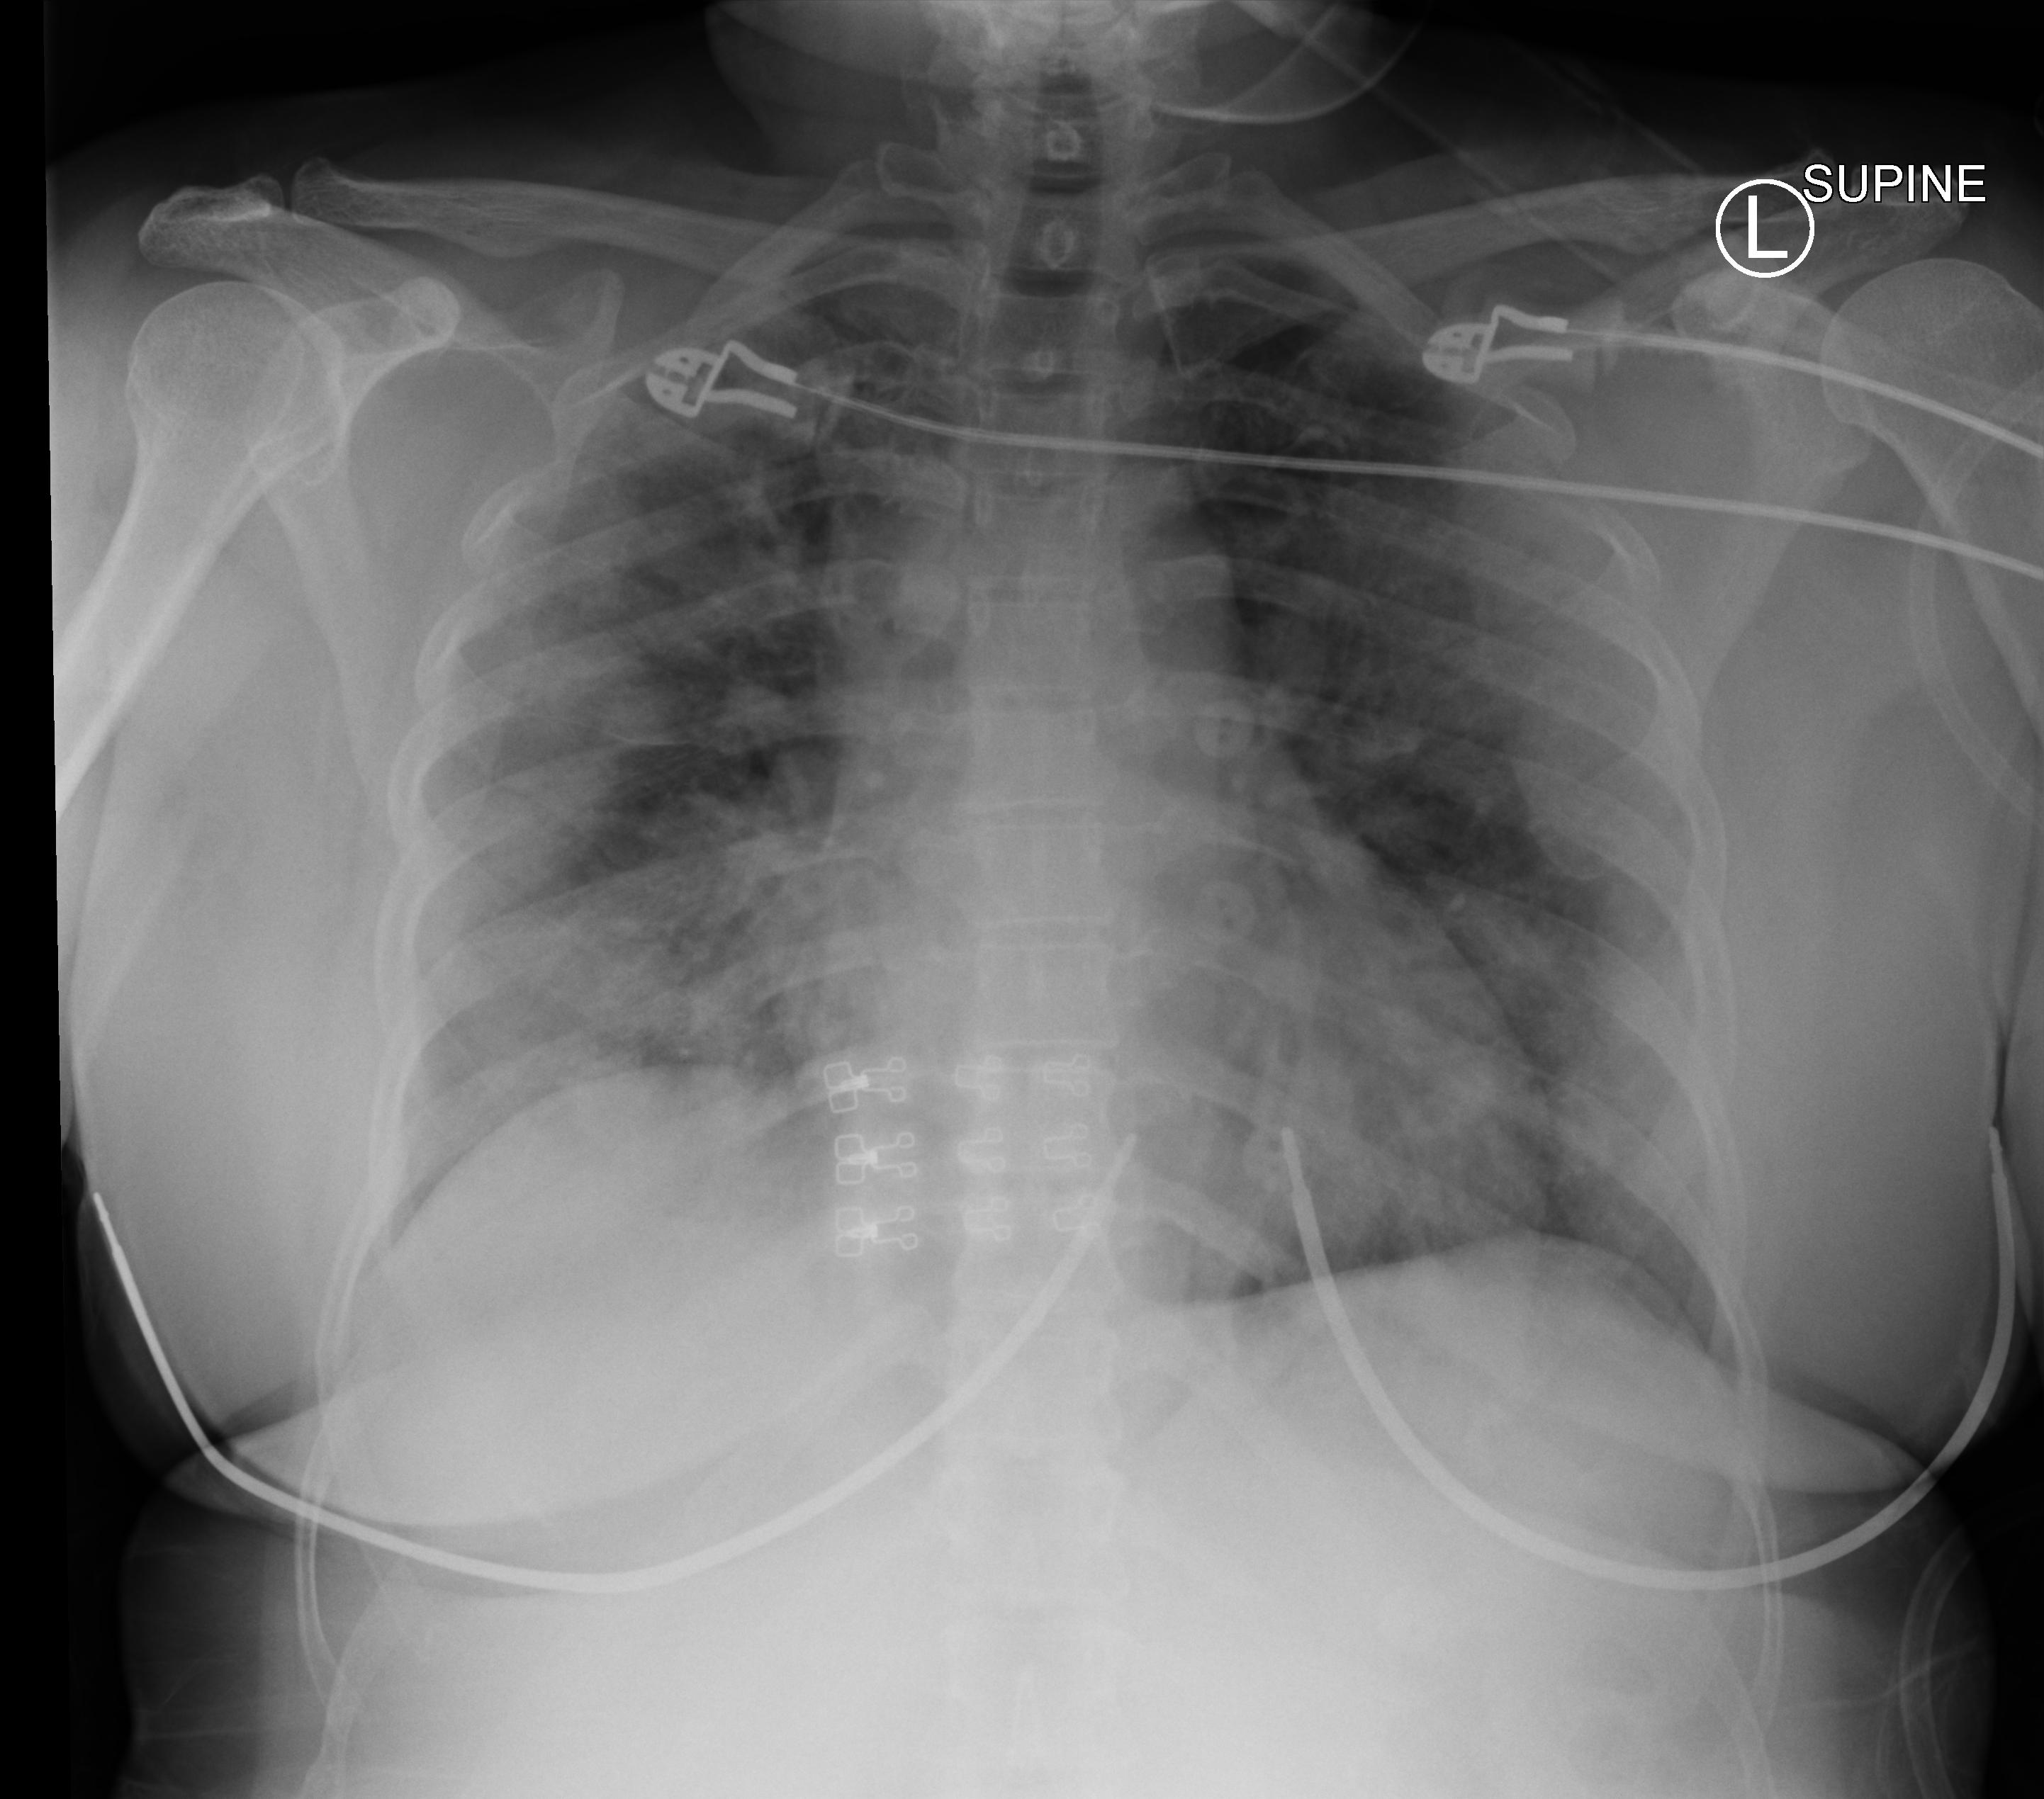
Portable chest radiograph, anteroposterior (AP) projection. Male patient hospitalised with COVID-19, age 18–59 years.
Hospital-stay facts (about this admission, not read from this image; timing relative to this image not recorded): admitted to intensive care during this hospital stay: yes.